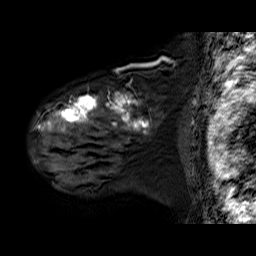
Breast MRI (dynamic contrast-enhanced), one sagittal slice. Slice 49 of 60 in the series (ordered by position). Dynamic contrast-enhanced series, time point 2 of 6 at this slice position (early post-contrast). 1.5 T. TE 6.3 ms, TR 32.9 ms. 256 × 256 image matrix, field of view 200 × 200 mm. Female patient. Case-level facts recorded for this patient, not image findings: setting: breast cancer imaged before/during neoadjuvant chemotherapy; receptor status: HER2-positive.
Annotated regions visible in this slice (semi-automatically segmented with operator editing):
- analysis volume of interest (the breast-tissue region the enhancement analysis was run in; not a lesion): bounding box <32,85,182,180> (left, top, right, bottom; pixels)
- tumour enhancement mask (voxels above the 100 % enhancement threshold inside the analysis volume of interest): <37,93,152,135>